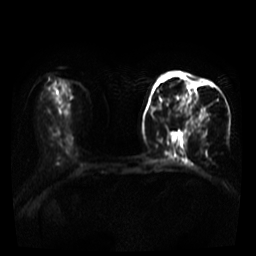
Breast MRI, one axial slice. Slice 13 of 39 in the series (ordered by position). Diffusion-weighted series; image 2 of 4 stored at this slice position (different b-values; order by instance number). 3 T. 5 mm slice thickness. 256 × 256 image matrix. Female patient.
Outlined on this slice (expert manual segmentation):
- tumour on diffusion-weighted imaging: bounding box (x1, y1, x2, y2) in pixels: (165, 81, 209, 121)